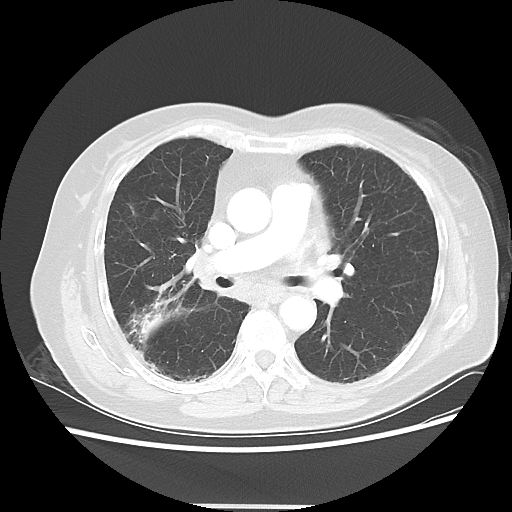
Chest CT, one axial slice. Reconstruction kernel LUNG. Lung window (W 1500 / L -600 HU). 5 mm slice thickness. 512 × 512 image matrix, field of view 360 × 360 mm. Female patient, age 72 years. From the clinical record (not read from this slice): clinical TNM (as recorded): T2 N1 M0; histopathological grade: G1.
Structures marked on this image (rectangle marked by the reading radiologist):
- lung tumour (recorded histology: adenocarcinoma): bounding box (x1, y1, x2, y2) in pixels: (139, 314, 163, 345)